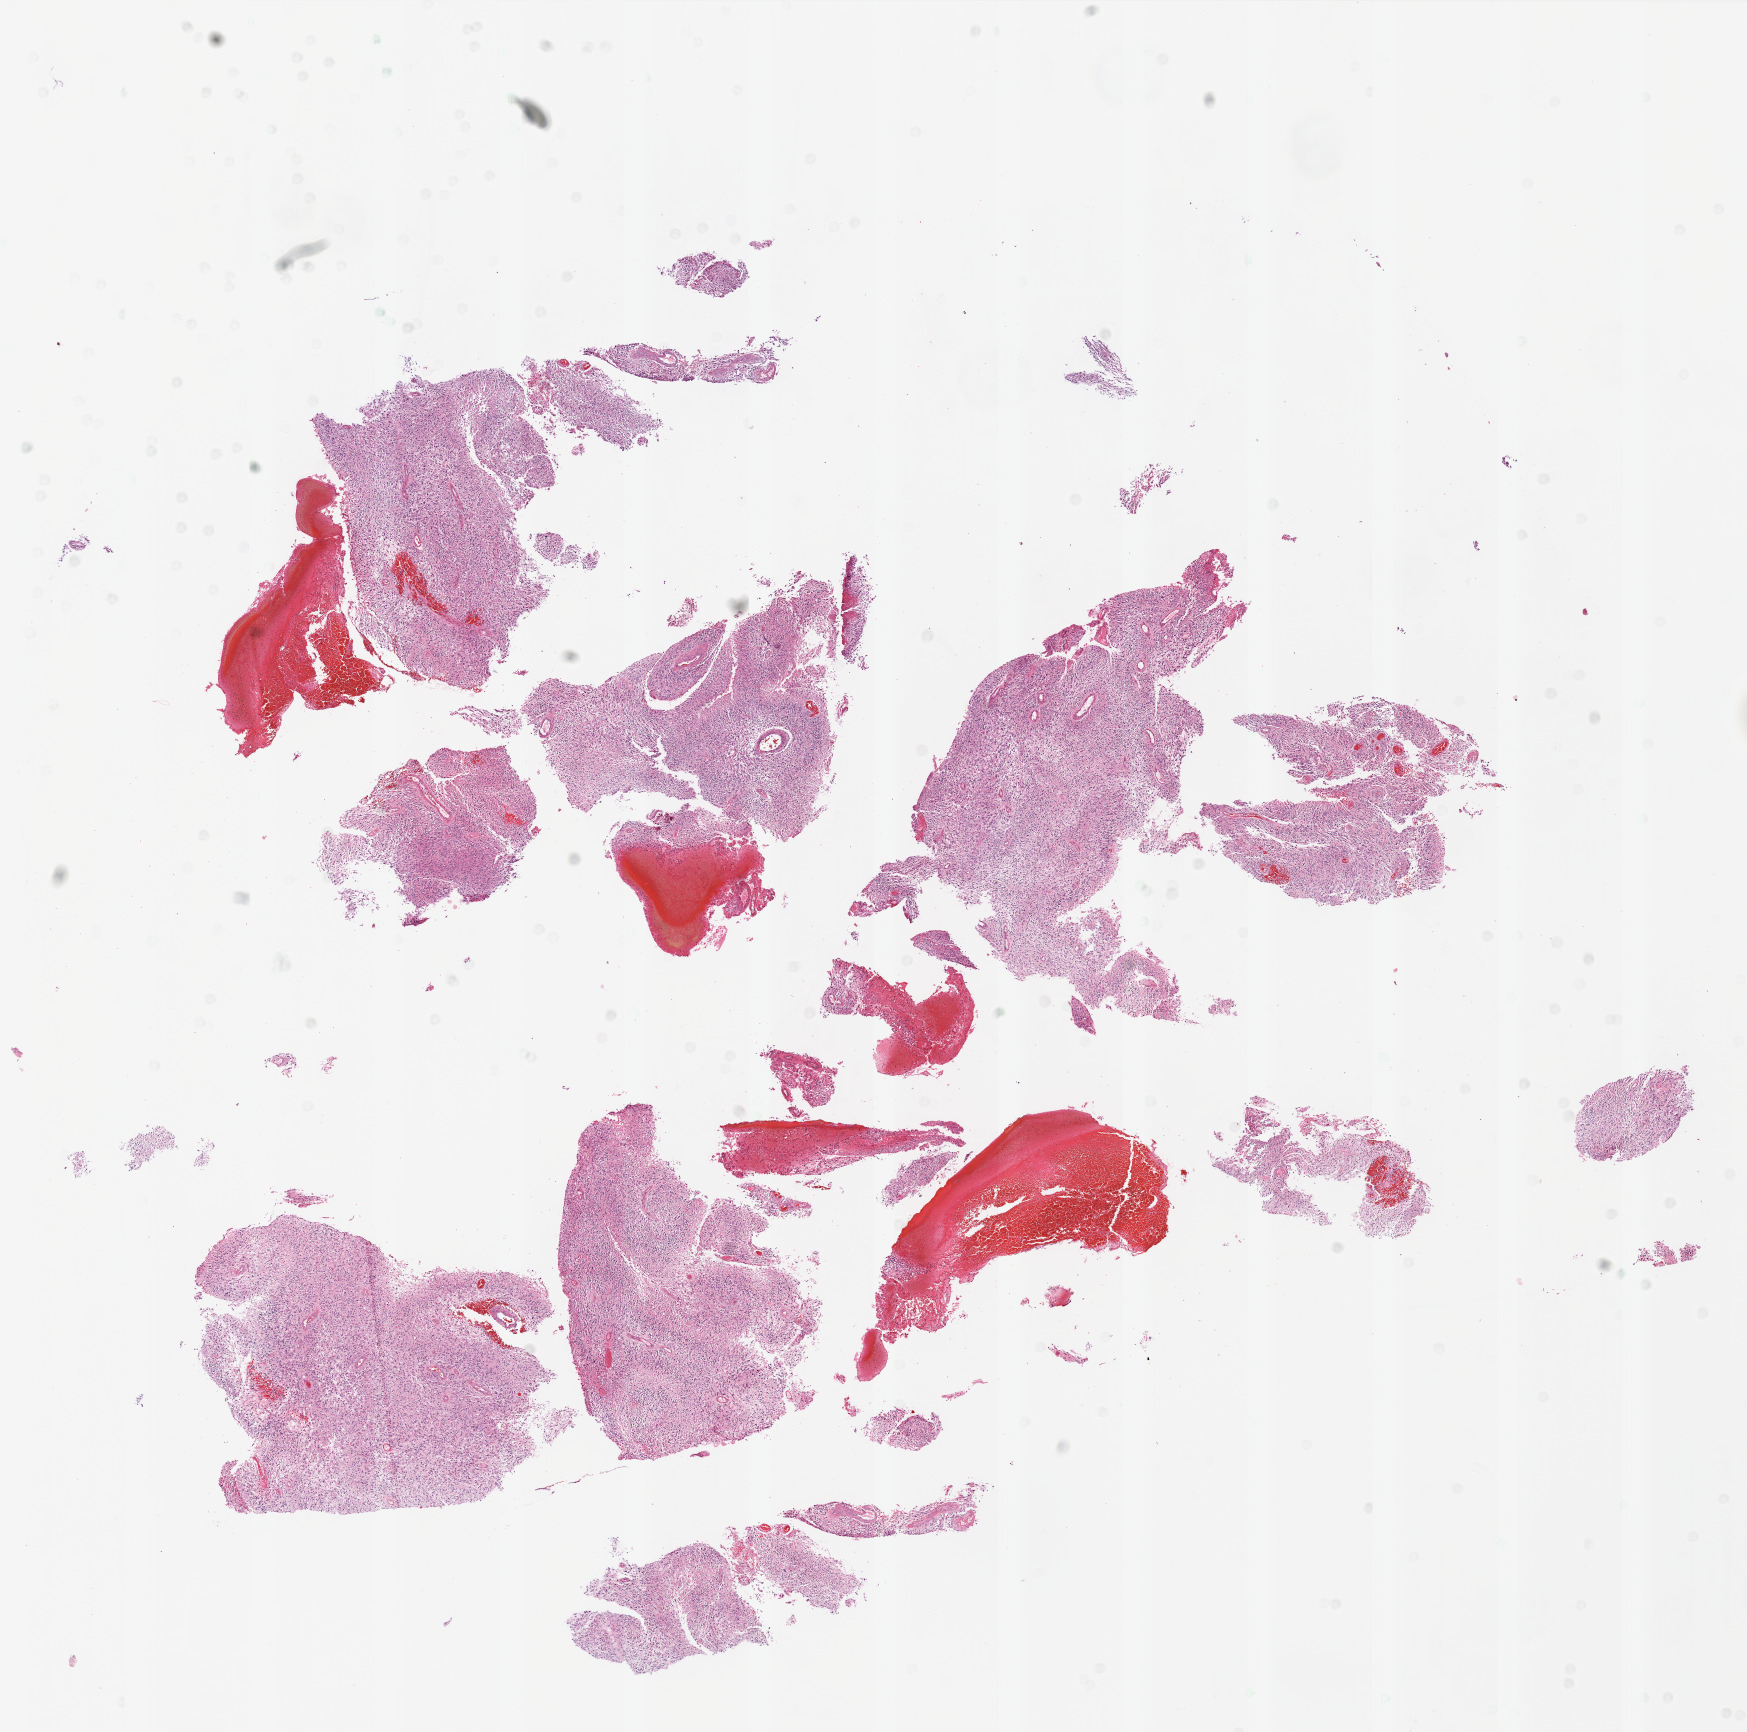
H&E whole-slide image, whole scanned area (about 14.0 x 13.9 mm) shown as a low-resolution overview. Formalin-fixed paraffin-embedded (FFPE) diagnostic section. Sample: primary tumour, brain. Female, age 72 years at initial diagnosis.
Histologic diagnosis: Glioblastoma.